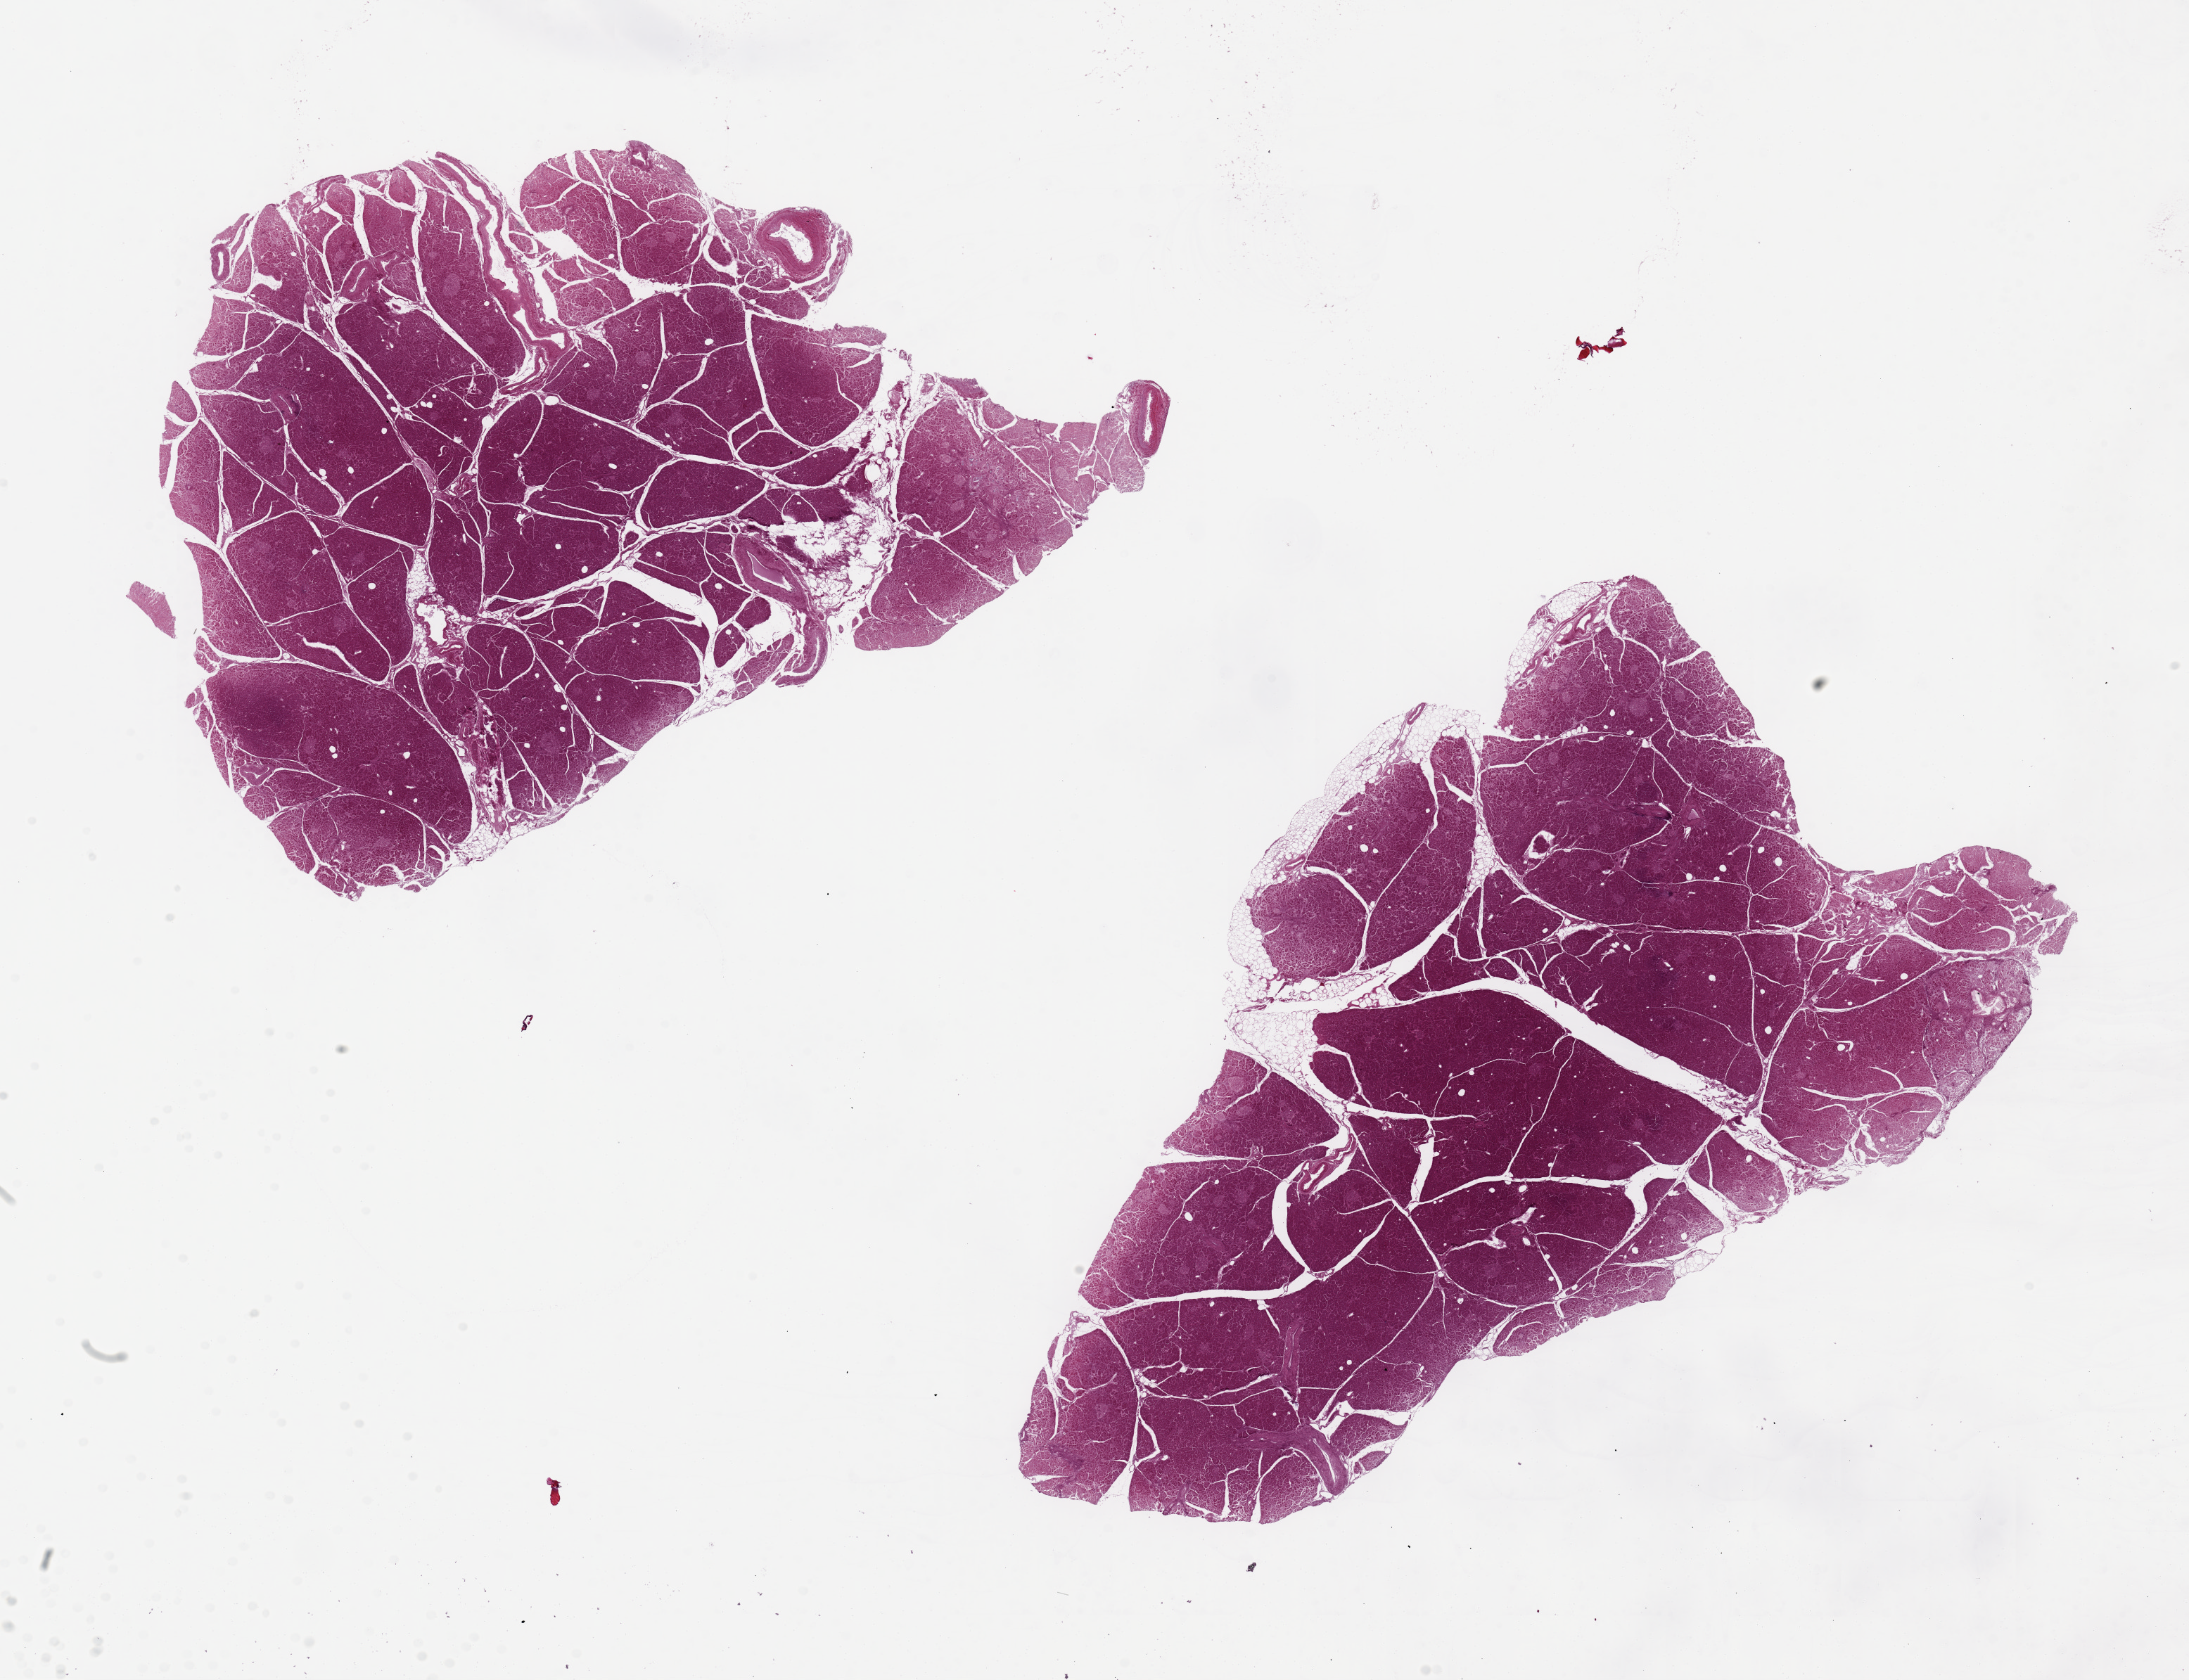
Whole-slide image, haematoxylin and eosin stain, whole scanned area (about 24.6 x 18.9 mm) shown as a low-resolution overview; PAXgene-fixed, paraffin-embedded tissue; section of pancreas (target tissue); tissue donor sample. Male donor.
Review note (as recorded): 2 pieces, 10.7x 7.6 & 12x7 mm; very little extraneous adipose.